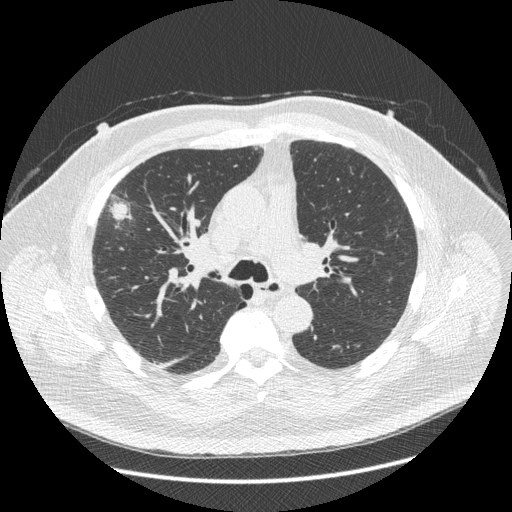
Chest CT (low-dose screening protocol), one axial image, third screening round (two years after baseline), lung window (W 1500 / L -600 HU), 1.25 mm slice thickness, slice 155 of 426 in the series, 512 × 512 image matrix, field of view 400 × 400 mm. Male participant, aged 66 years at enrolment. Current smoker at enrolment.
- Expert reader's lesion annotation, bounding box (x1, y1, x2, y2) in pixels: (86, 178, 145, 264).
- The exam's reader record, not a measurement of the box and not confirmed to be the same lesion: non-calcified nodule or mass ≥4 mm, right upper lobe, 48 × 25 mm, spiculated (stellate) margins, soft tissue attenuation, pre-existing on the prior screen: no.